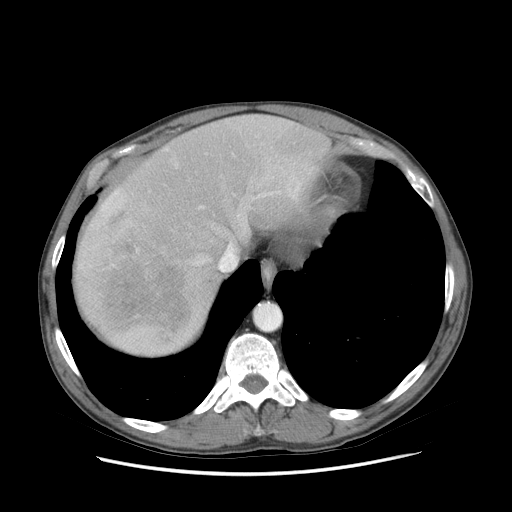
Contrast-enhanced abdominal CT (liver protocol), one axial slice; slice 66 of 89 in the series (ordered by position); reconstruction kernel STANDARD; 140 kVp; soft-tissue window (W 400 / L 40 HU); 2.5 mm slice thickness; 512 × 512 image matrix. From the clinical record (not read from this slice): diagnosis: hepatocellular carcinoma (patient treated with transarterial chemoembolisation; whether this scan precedes or follows treatment is not stated here); TNM stage (as recorded): Stage-IIIB; Child-Pugh class: A; tumour differentiation: moderately differentiated; tumour nodularity: multinodular.
Annotated regions visible in this slice (semi-automatic segmentation, software-assisted and operator-edited):
- abdominal aorta: bounding box [x1, y1, x2, y2] px = [256, 305, 280, 329]
- liver parenchyma outside the tumour (the mass and vessels are separate outlines, so this box may not span the whole liver): [74, 114, 330, 354]
- mass: [90, 208, 196, 335]
- liver vessels: [80, 182, 300, 267]